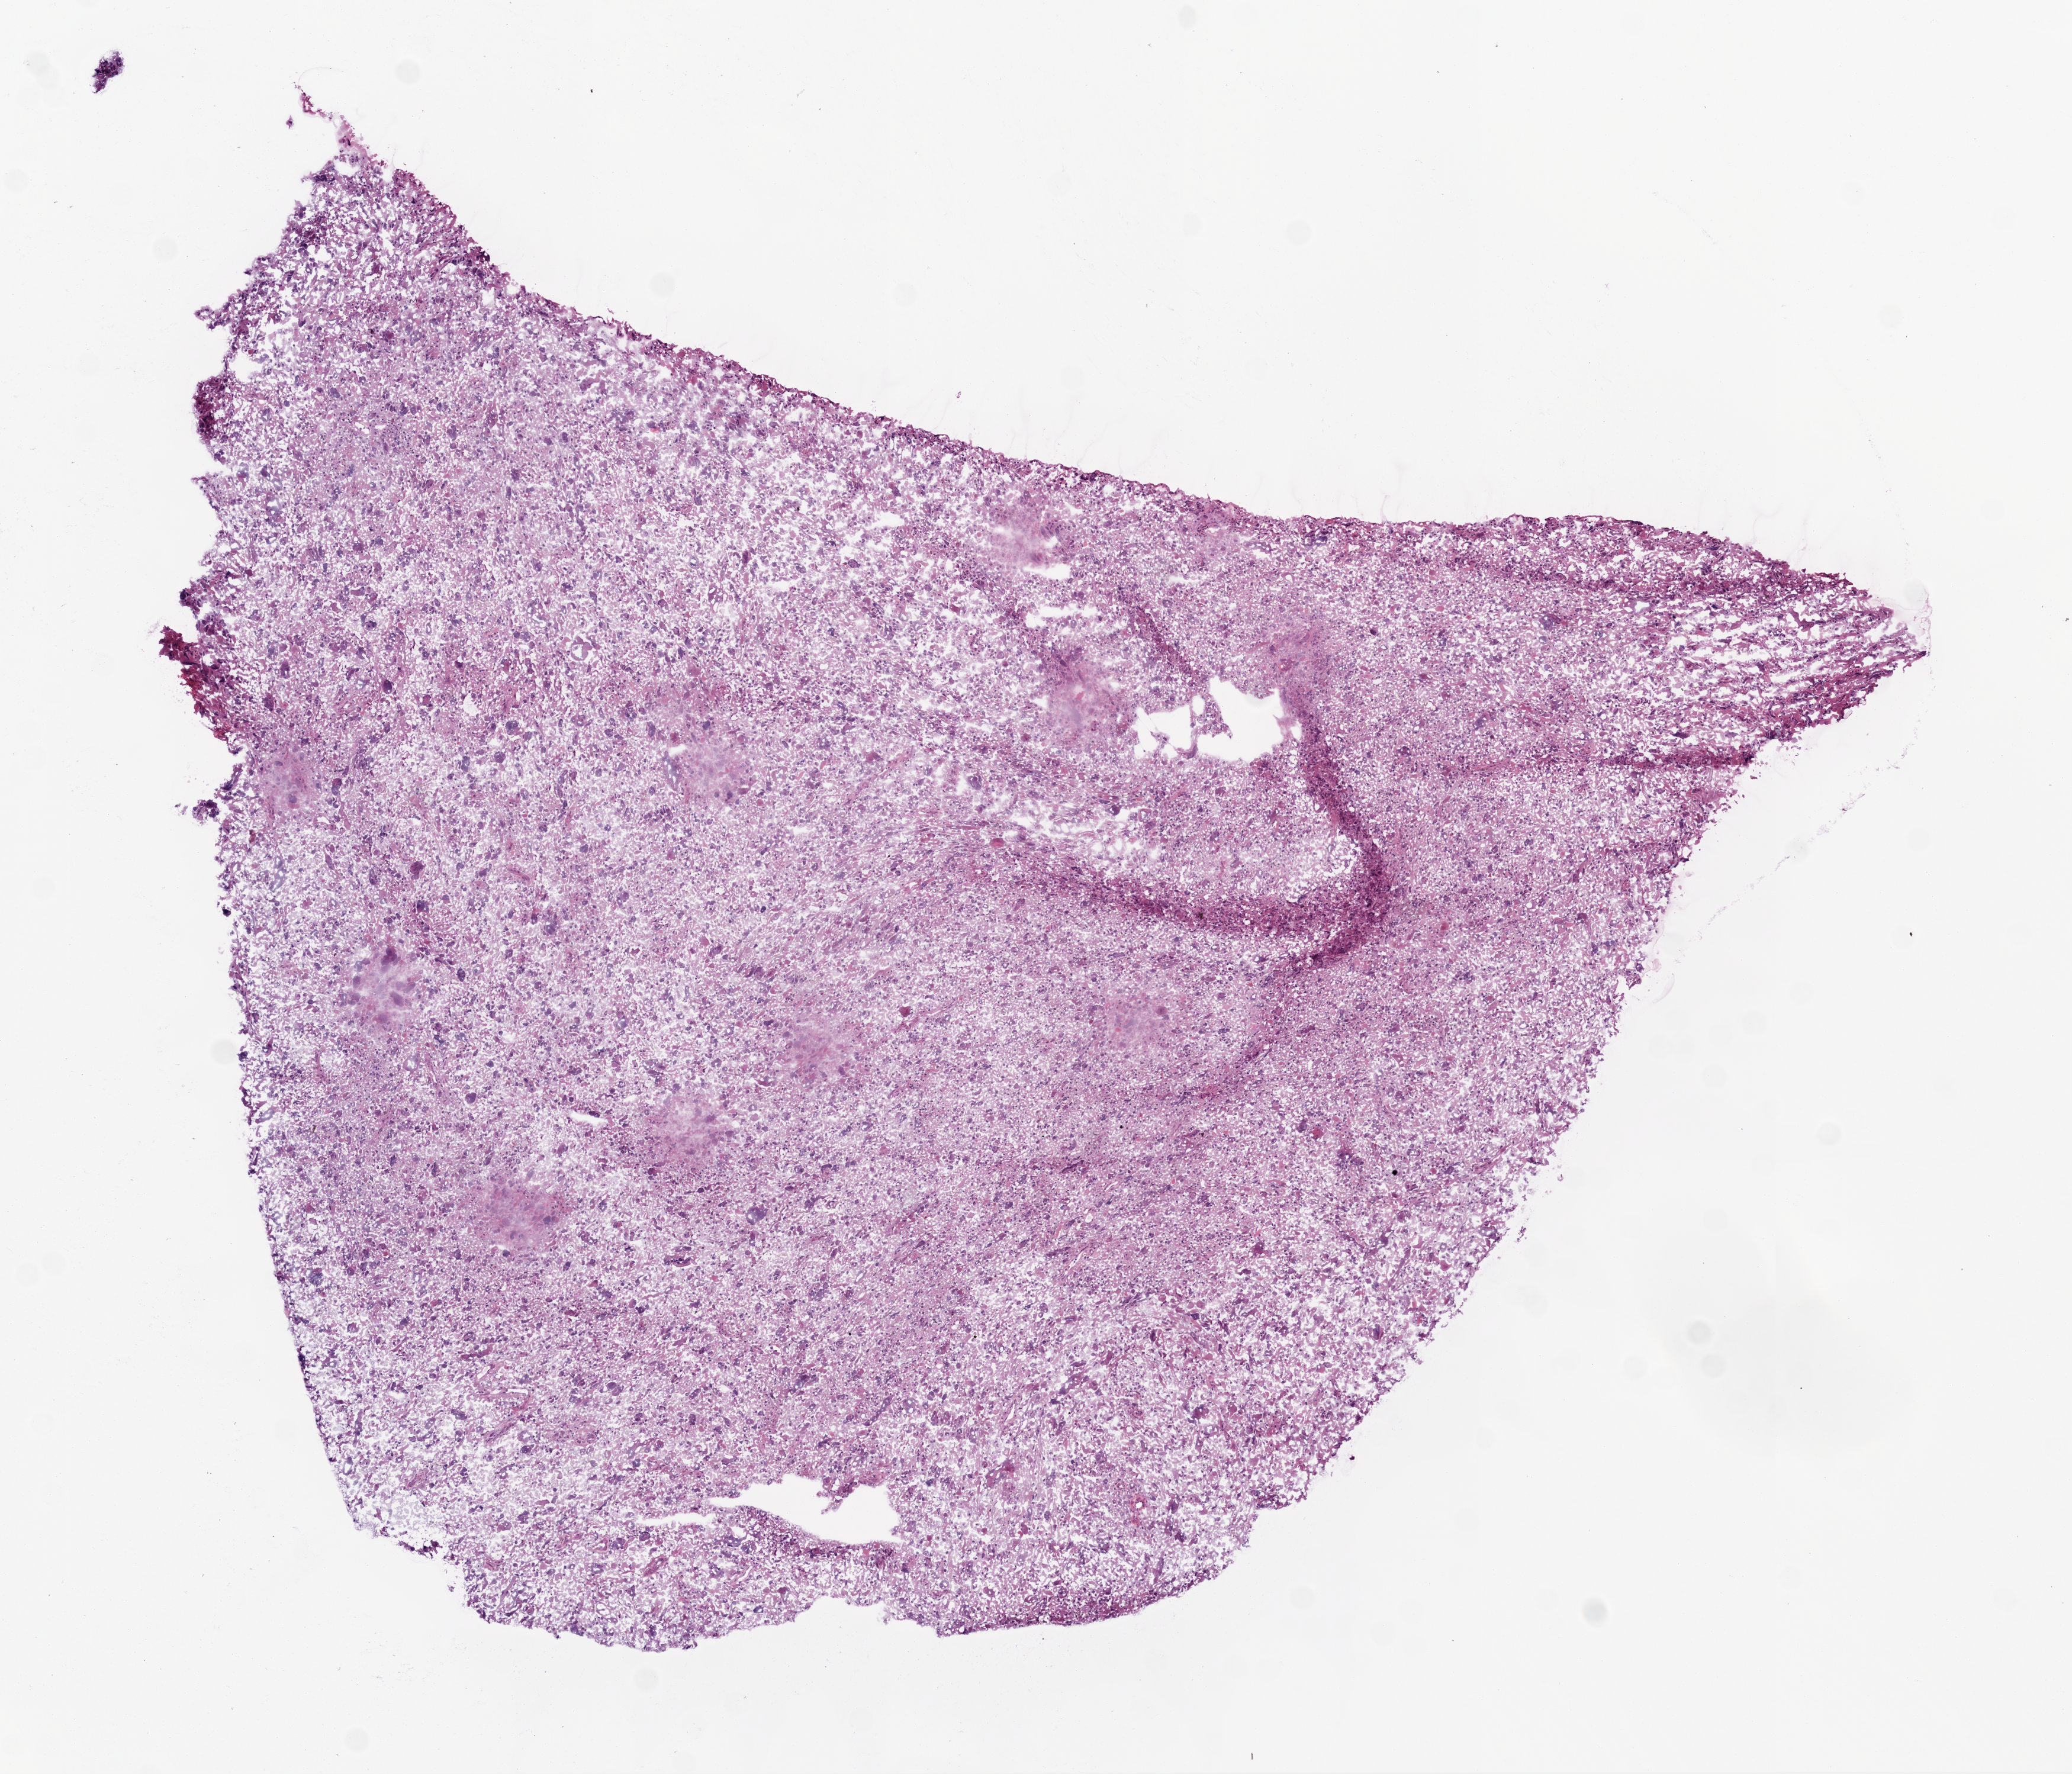
Hematoxylin and eosin (H&E) stained whole-slide image, shown as a low-resolution overview of the whole scanned area (about 7.0 x 6.0 mm, slide scanned at 20x), frozen section, brain, primary tumour sample. Male patient; age at initial diagnosis 37 years. Composition of this section per pathologist review: tumour cells 100%, tumour nuclei 80%, normal cells 0%, stromal cells 0%, necrosis 0%.
Histologic diagnosis: Glioblastoma.